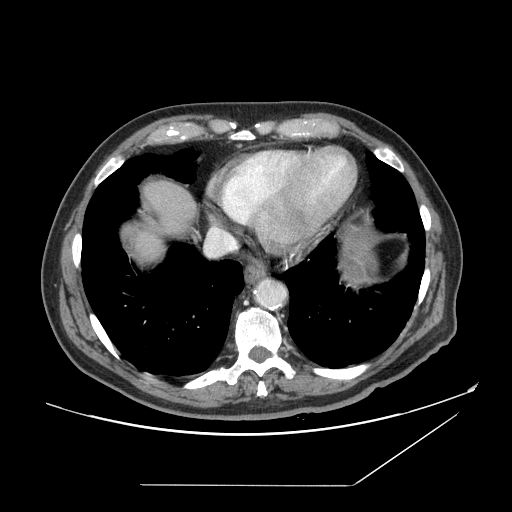
Contrast-enhanced abdominal CT, one axial slice; position 143 of 166 along the scan axis; 120 kVp; intravenous contrast given; soft-tissue window (W 400 / L 40 HU); 2.5 mm slice thickness; 512 × 512 image matrix. Male patient, age 80 years. From the clinical record (not read from this slice): diagnosis: colorectal cancer liver metastases, imaged before liver resection; multiple liver metastases: no; largest metastasis: 2.2 cm; chemotherapy before resection: no.
Annotated regions visible in this slice (expert manual segmentation):
- liver: bounding box [x1, y1, x2, y2] px = [120, 181, 198, 267]
- planned liver remnant (the part of the liver to remain after resection): [119, 181, 197, 257]